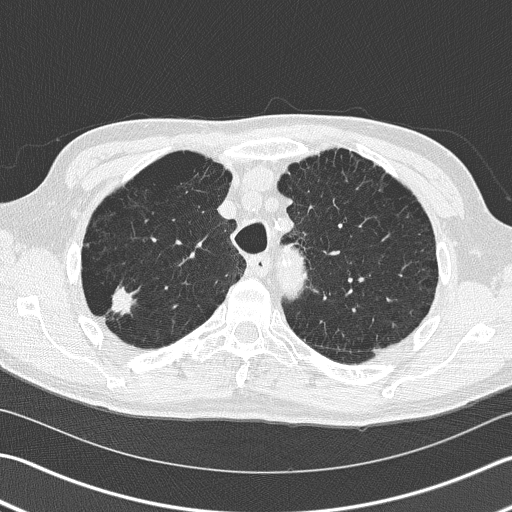
Axial slice from a low-dose chest CT screening exam, first (baseline) screen, lung window (W 1500 / L -600 HU), 120 kVp. Male participant, aged 66 years at enrolment. Current smoker at enrolment.
- Expert-annotated lung lesion, box from (x=84, y=268) to (x=144, y=340) px.
- Screening reader's record for this exam (one nodule recorded; not confirmed to be the boxed lesion): non-calcified nodule or mass ≥4 mm, right upper lobe, 39 × 23 mm, spiculated (stellate) margins, soft tissue attenuation.
- Lung cancer was diagnosed 36 days after this screen: squamous cell carcinoma, NOS, right upper lobe, poorly differentiated (G3), stage IB (AJCC 6th edition), 23 mm at pathology.